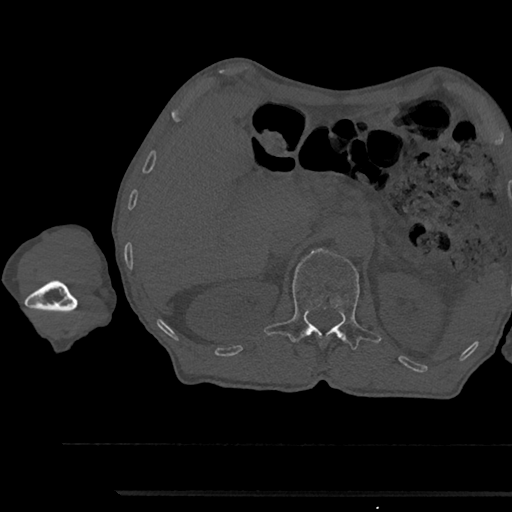
CT including the spine, one axial slice; position 649 of 797 along the scan axis; reconstruction kernel Br40s/3; 120 kVp; bone window (W 1800 / L 400 HU); 0.5 mm slice thickness; 512 × 512 image matrix, field of view 367 × 367 mm. Patient: male, 79 years. Case-level facts recorded for this patient, not image findings: primary cancer: prostate.
Outlined on this slice (semi-automatic segmentation, software-assisted and operator-edited):
- L1 vertebra: bounding box (x1, y1, x2, y2) in pixels: (264, 248, 381, 350)